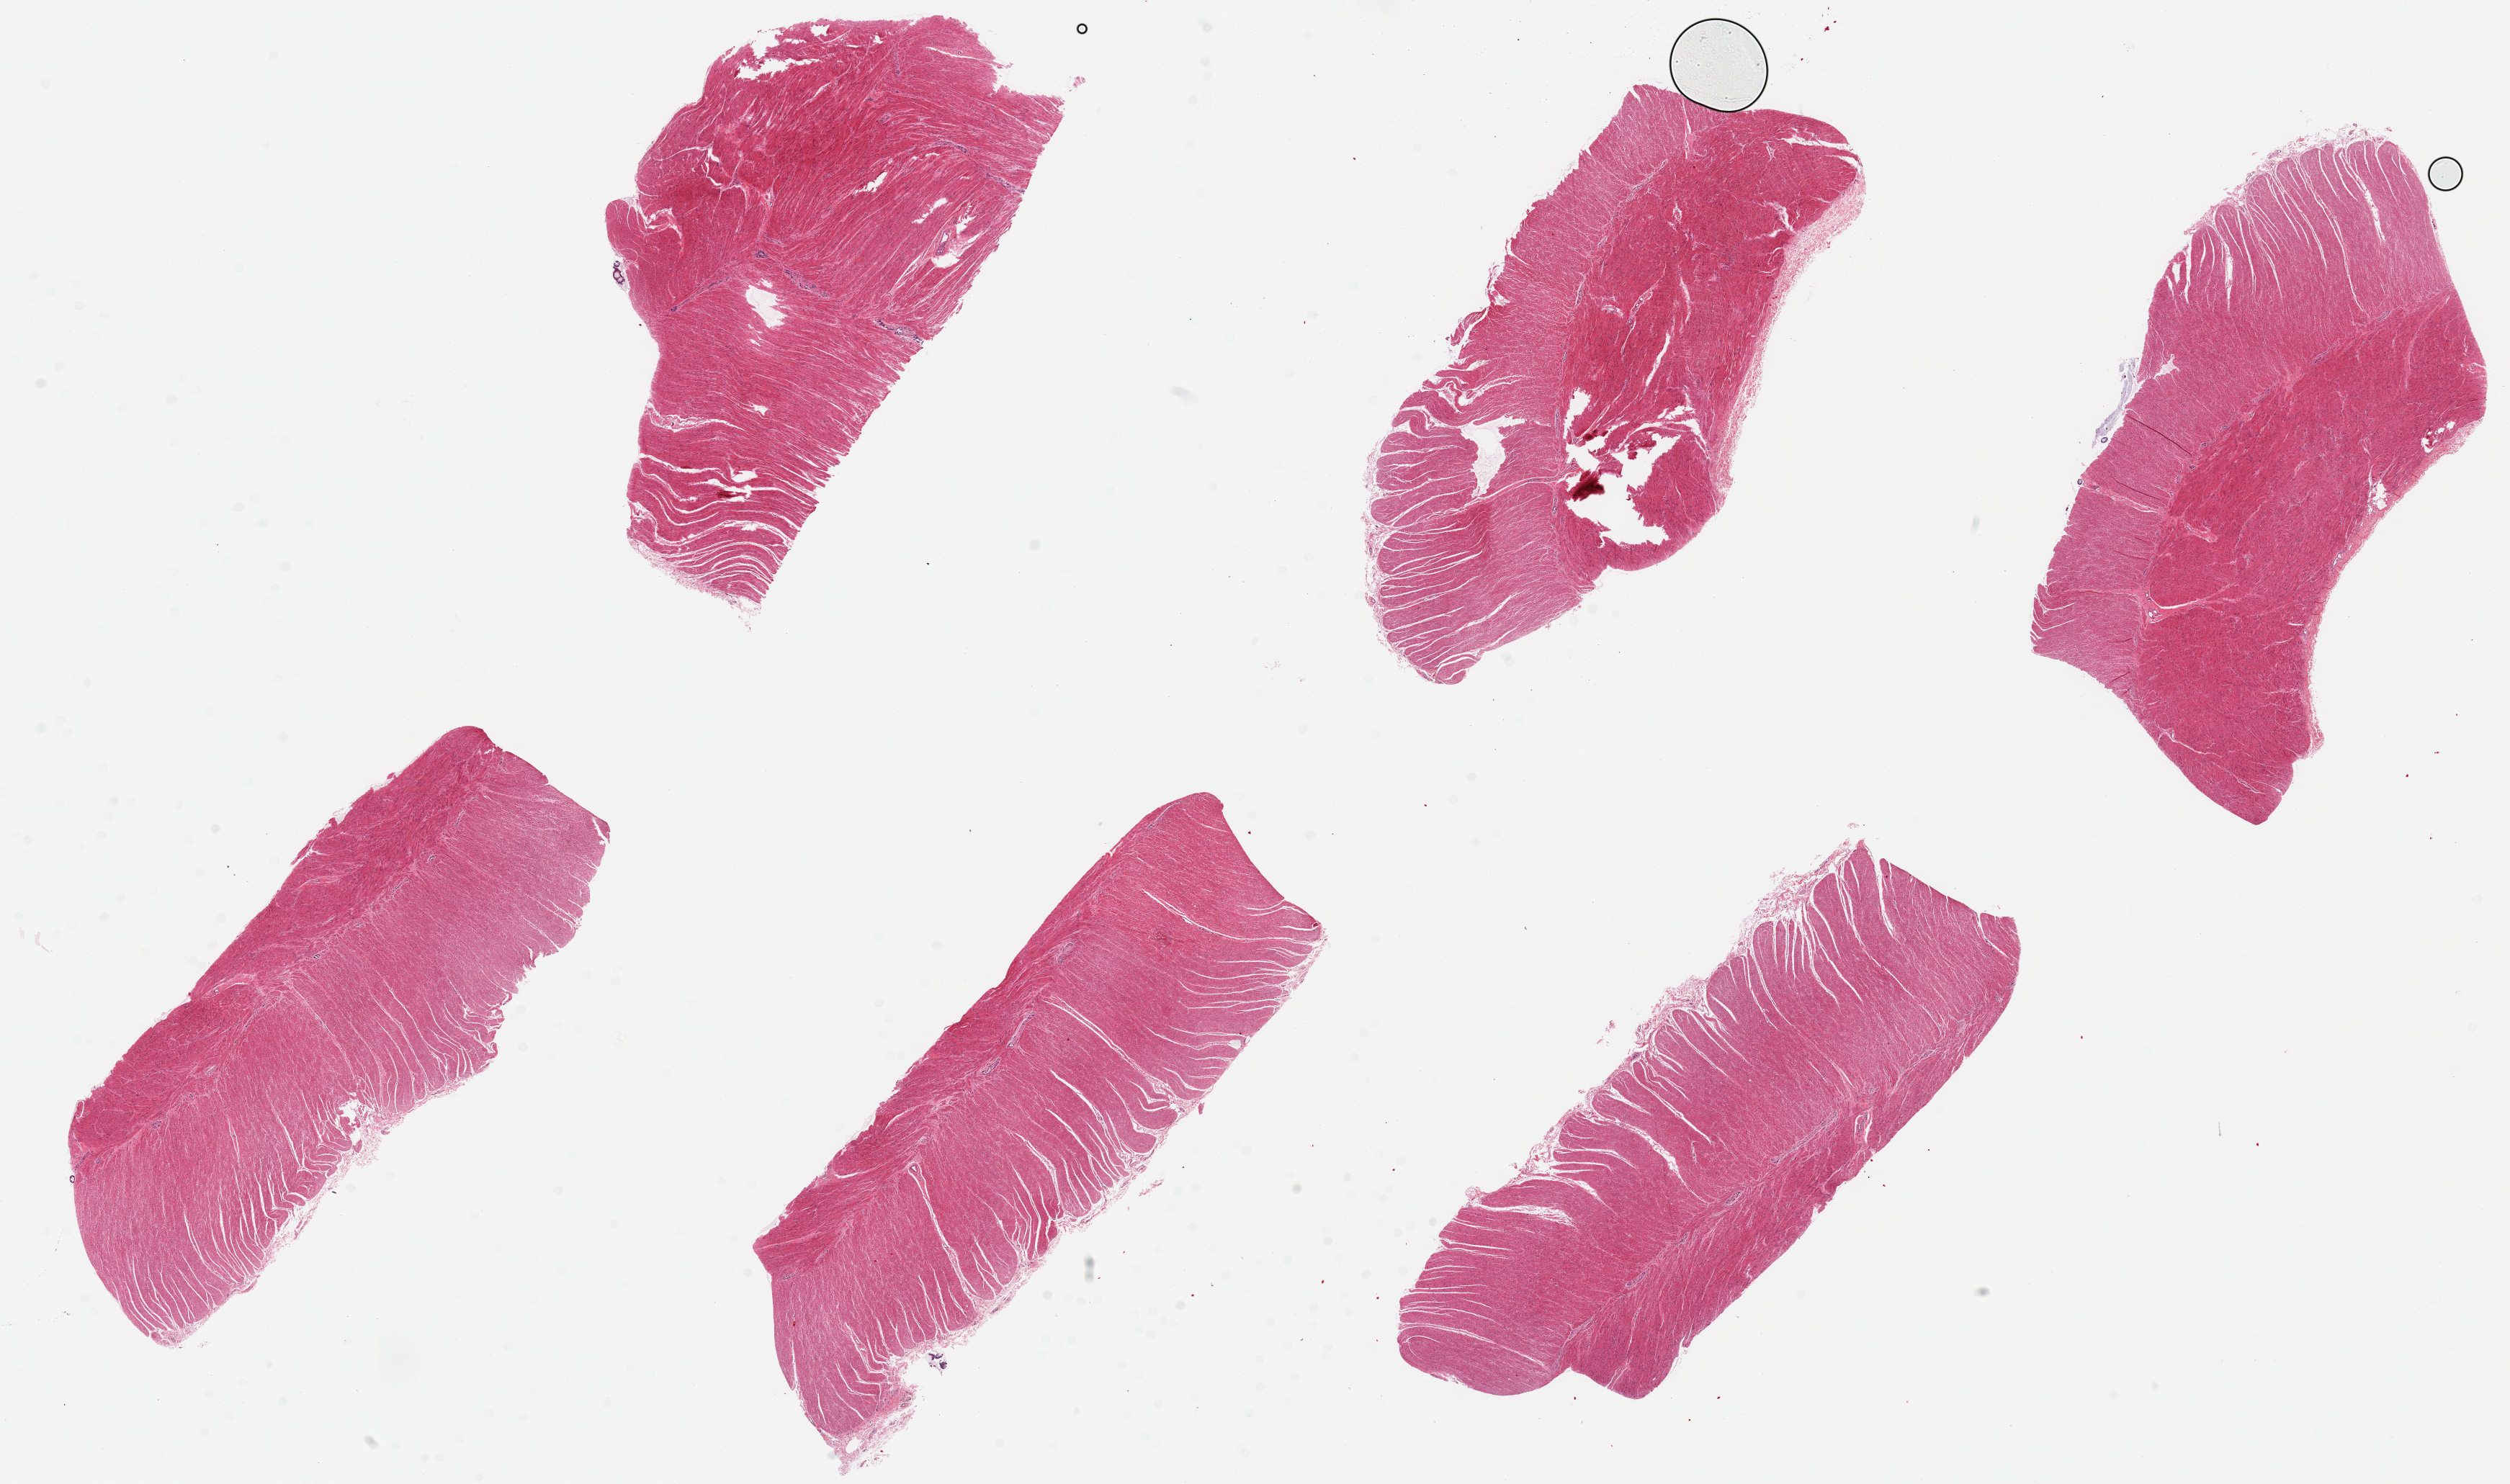
Whole-slide image, haematoxylin and eosin stain, brightfield — shown as a low-resolution overview of the whole scanned area (about 27.6 x 16.3 mm, slide scanned at 20x). PAXgene-fixed, paraffin-embedded tissue. Sampled site (target tissue): sigmoid colon. Tissue donor sample. Male donor.
• review note (as recorded): 6 pieces up to ~8x3mm, all muscularis, excellent specimens